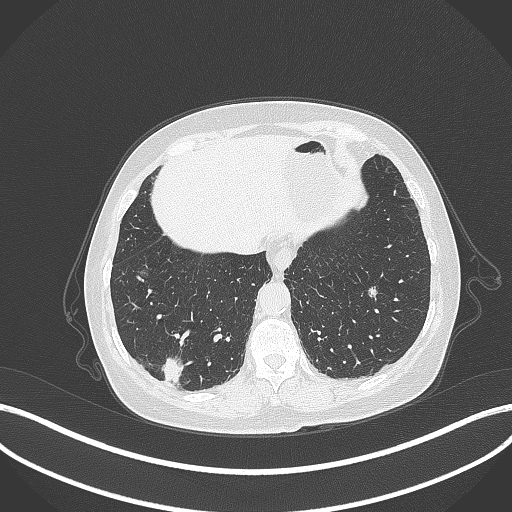
Chest CT, one axial slice; slice 63 of 333 in the series (ordered by position); reconstruction kernel B70f; lung window (W 1500 / L -600 HU); 1 mm slice thickness; 512 × 512 image matrix, field of view 400 × 400 mm. Female patient, age 69 years. Case-level facts recorded for this patient, not image findings: clinical TNM (as recorded): T1b N0 M0.
Outlined on this slice (bounding box drawn by a radiologist):
- lung tumour (recorded histology: adenocarcinoma): bounding box <157,352,185,385> (left, top, right, bottom; pixels)